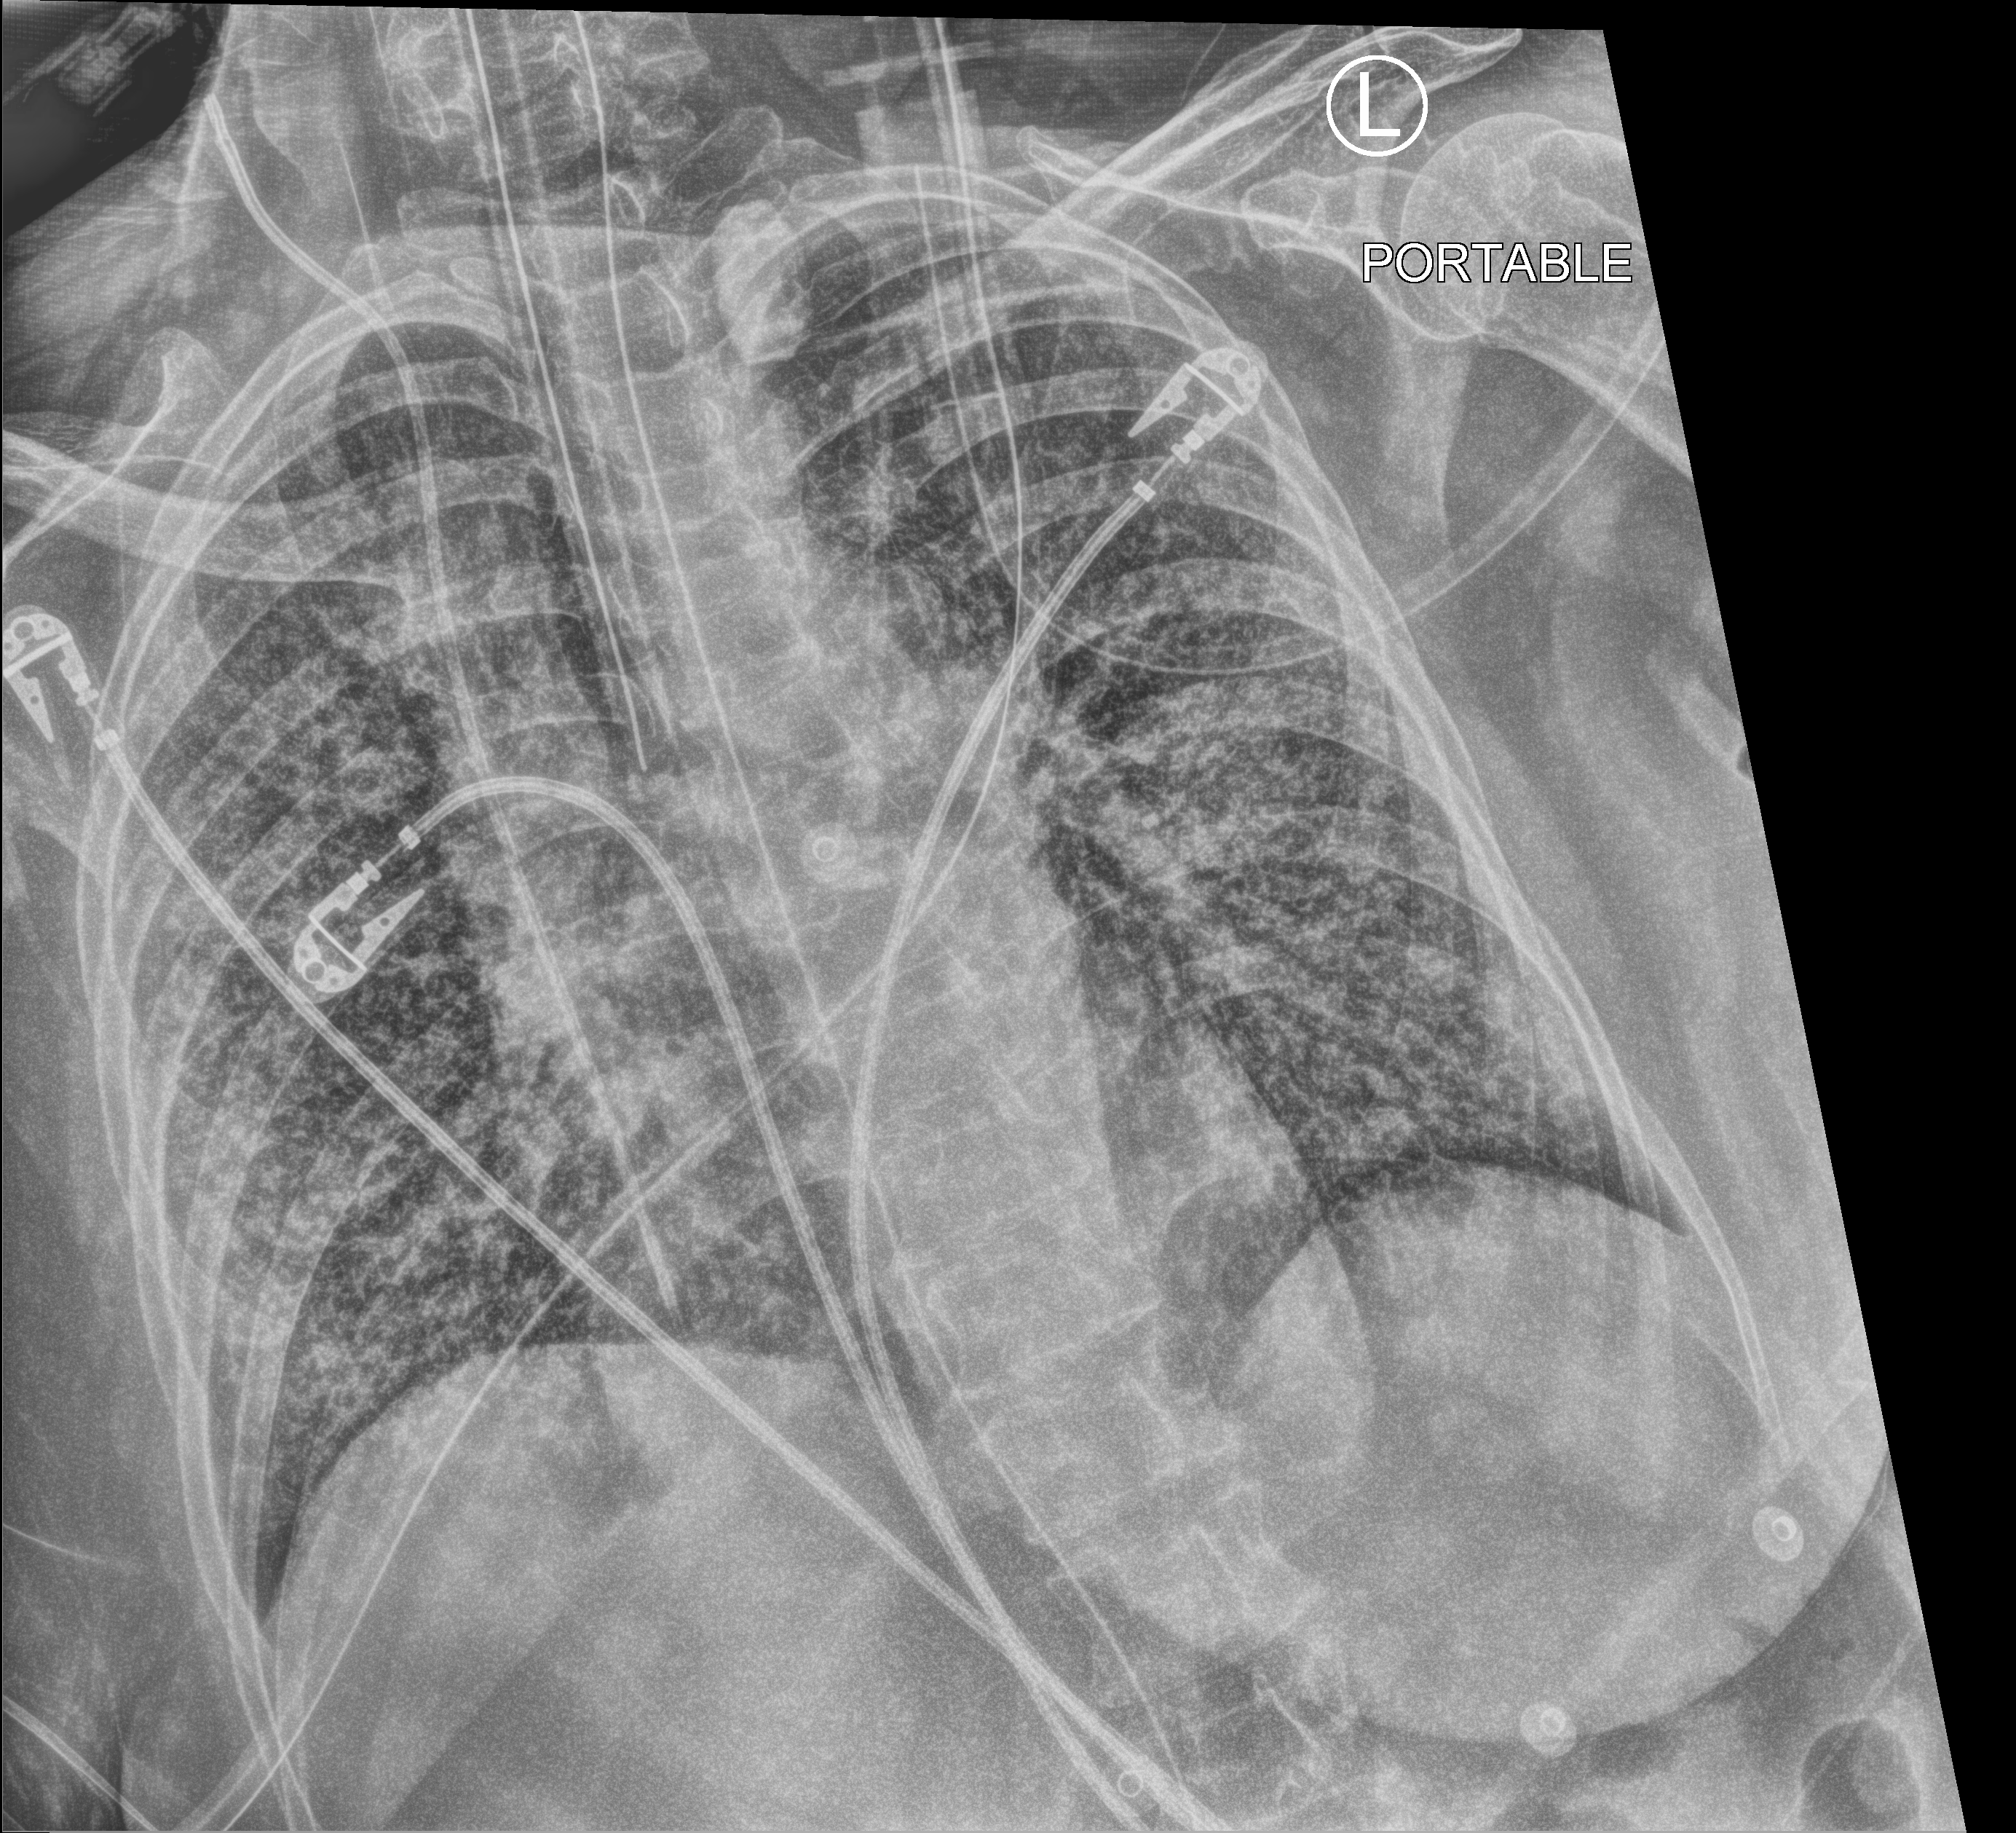
Chest X-ray (portable); anteroposterior (AP) projection. Patient hospitalised with COVID-19; female, aged 60–74 years.
From the hospital-stay record, not from the radiograph (when in the stay this image was taken is not recorded): hypertension (admission record): no.